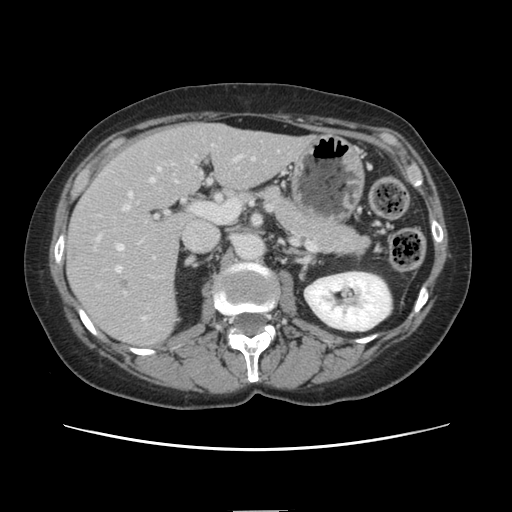
Contrast-enhanced abdominal CT, one axial slice. Intravenous contrast given. Soft-tissue window (W 400 / L 40 HU). 2.5 mm slice thickness. 512 × 512 image matrix, field of view 350 × 350 mm. Female patient, age 63 years. Case-level facts recorded for this patient, not image findings: diagnosis: colorectal cancer liver metastases, imaged before liver resection; multiple liver metastases: yes; largest metastasis: 3.2 cm; disease in both lobes: yes.
Outlined on this slice (manually delineated by an expert):
- hepatic veins: bounding box [x1, y1, x2, y2] px = [115, 168, 160, 273]
- liver: [68, 125, 307, 347]
- planned liver remnant (the part of the liver to remain after resection): [175, 125, 308, 191]
- portal vein (with intrahepatic branches): [97, 177, 153, 319]
- liver metastasis: [118, 279, 130, 290]
- liver metastasis: [71, 253, 78, 259]